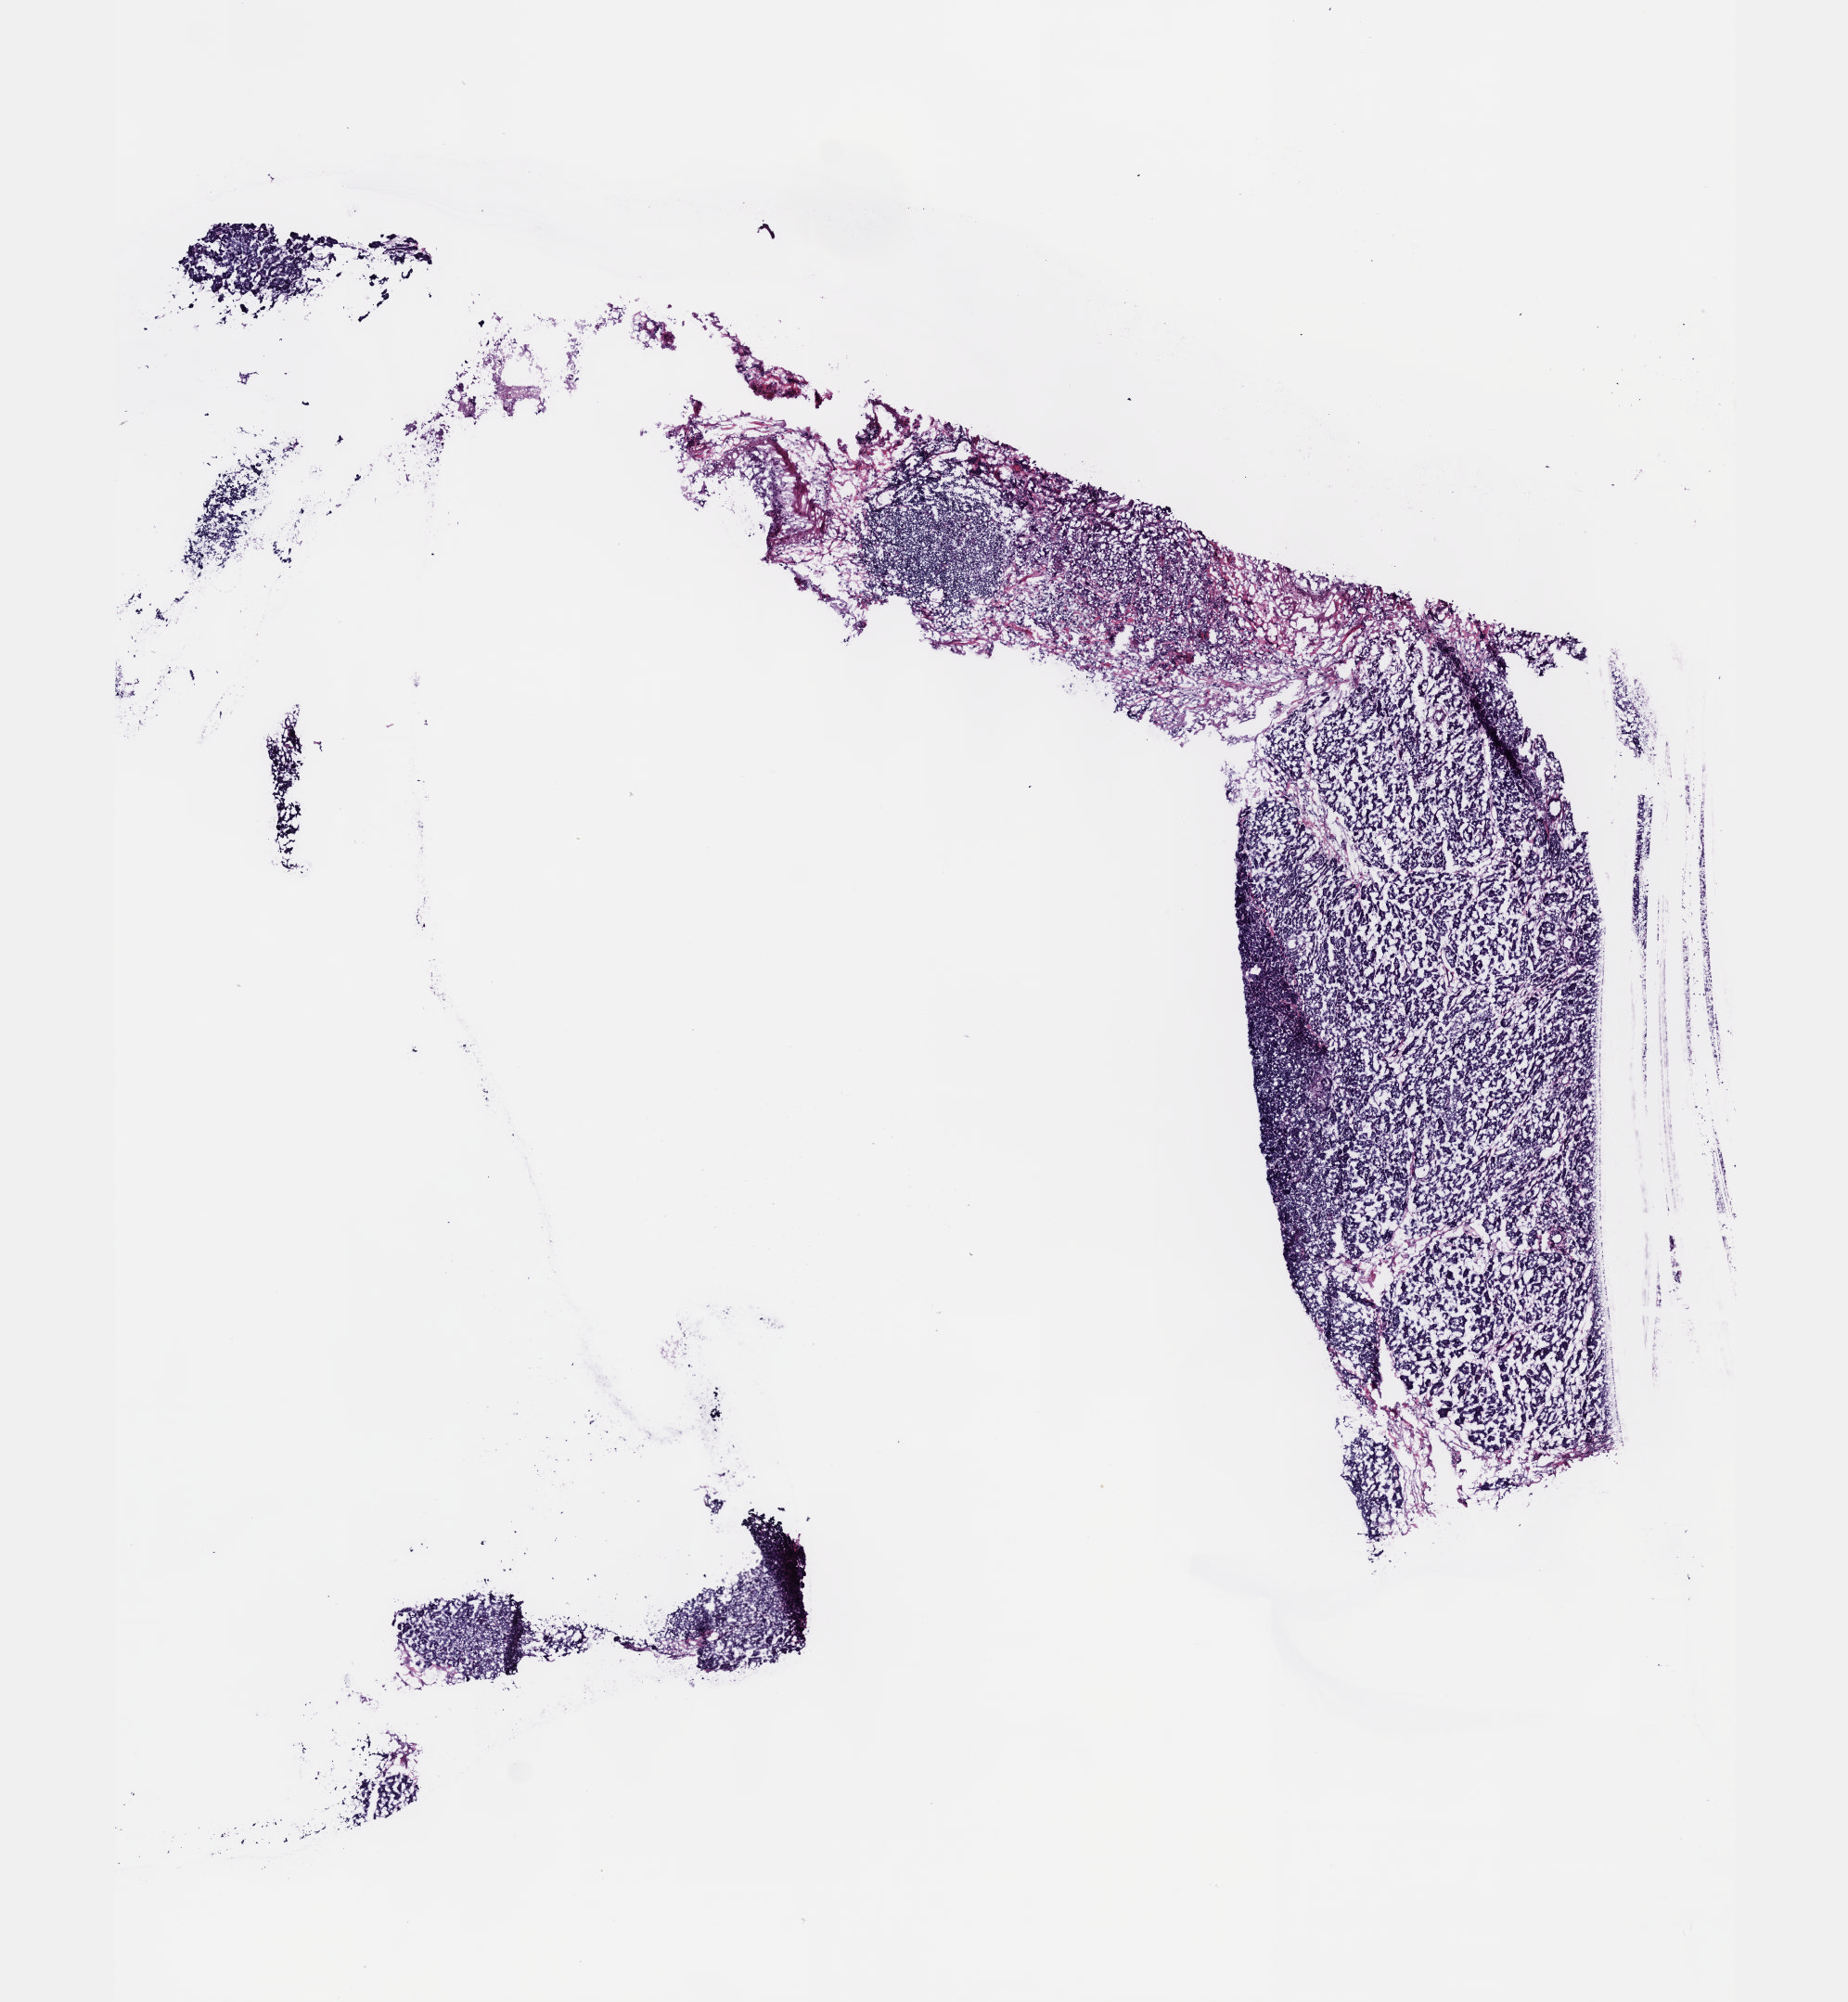
Whole-slide histology image, Hematoxylin and eosin (H&E) stained, a low-resolution overview of the entire scanned area, about 8.0 x 8.7 mm. Frozen section from the top of the tissue portion. Sample: primary tumour, bile duct. Female patient. Histologic grade: G2 (moderately differentiated). Slide review estimates, as recorded: tumour cells 100%, tumour nuclei 75%, normal cells 0%, stromal cells 0%, necrosis 0%. Inflammatory infiltration, as recorded: lymphocyte infiltration 2%, monocyte infiltration 0%, neutrophil infiltration 0%.
Pathologic diagnosis: Cholangiocarcinoma (extrahepatic bile duct). AJCC pathologic stage: IIB (7th edition).